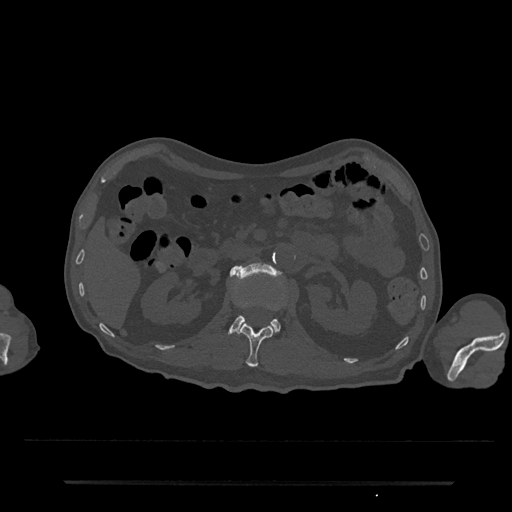
CT including the spine, one axial slice; slice 102 of 797 in the series (ordered by position); reconstruction kernel Br40s/3; 120 kVp; bone window (W 1800 / L 400 HU); 0.5 mm slice thickness; 512 × 512 image matrix, field of view 427 × 427 mm. Male patient, age 74 years. Case-level facts recorded for this patient, not image findings: primary cancer: prostate.
Structures marked on this image (semi-automatically segmented with operator editing):
- L1 vertebra: box from (x=240, y=323) to (x=274, y=368) px
- L2 vertebra: (x=228, y=262)–(x=280, y=334)